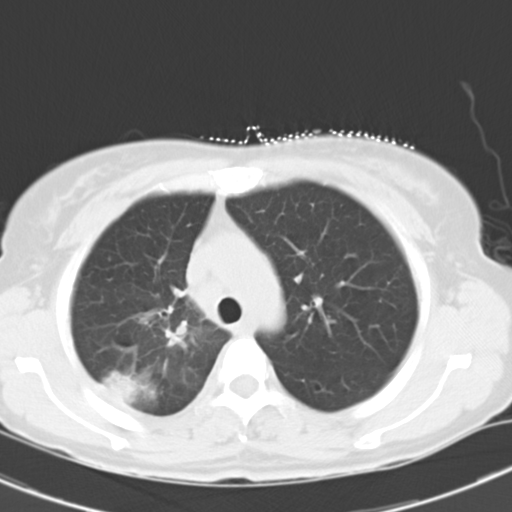
Chest CT, one axial slice; position 22 of 29 along the scan axis; reconstruction kernel B40f; lung window (W 1500 / L -600 HU); 8 mm slice thickness; 512 × 512 image matrix, field of view 300 × 300 mm. Patient: female, 47 years. Case-level facts recorded for this patient, not image findings: clinical TNM (as recorded): T1c N3 M0.
Outlined on this slice (rectangle marked by the reading radiologist):
- lung tumour (recorded histology: adenocarcinoma): bounding box [x1, y1, x2, y2] px = [105, 371, 140, 403]